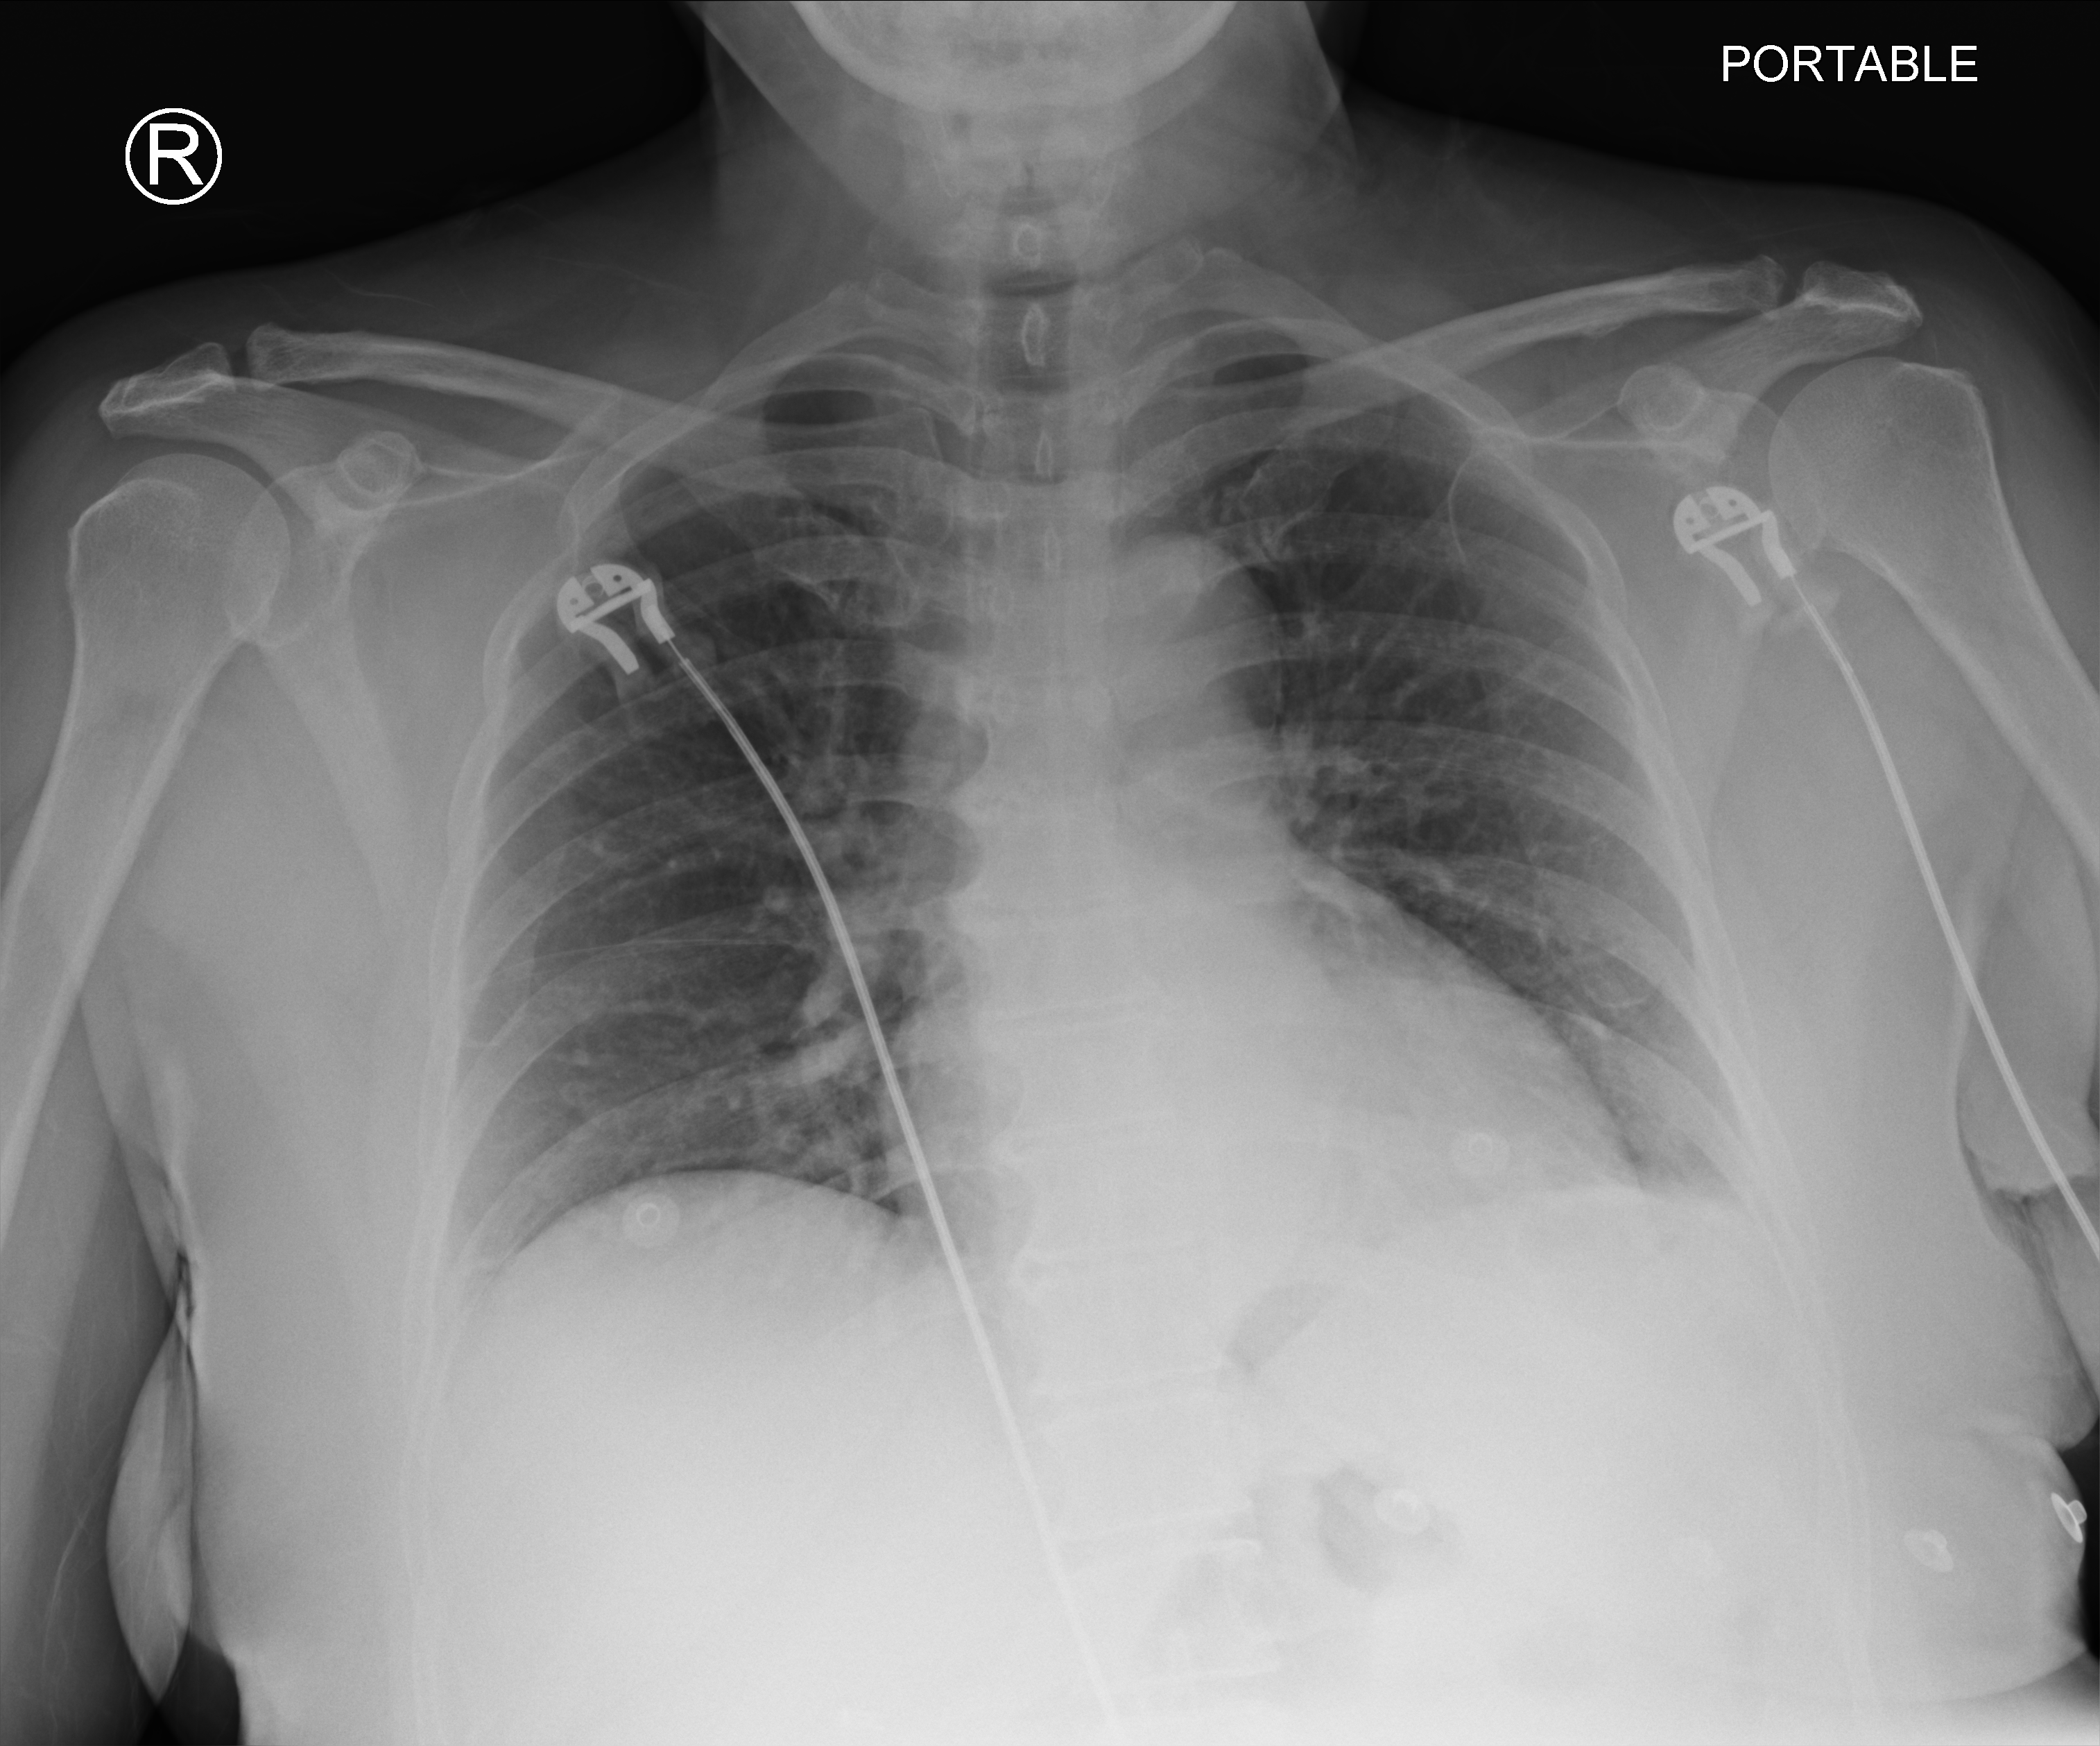
Chest X-ray (portable). Female patient hospitalised with COVID-19, age 18–59 years.
From the hospital-stay record, not from the radiograph (when in the stay this image was taken is not recorded):
- mechanically ventilated during this hospital stay: no
- admitted to intensive care during this hospital stay: no